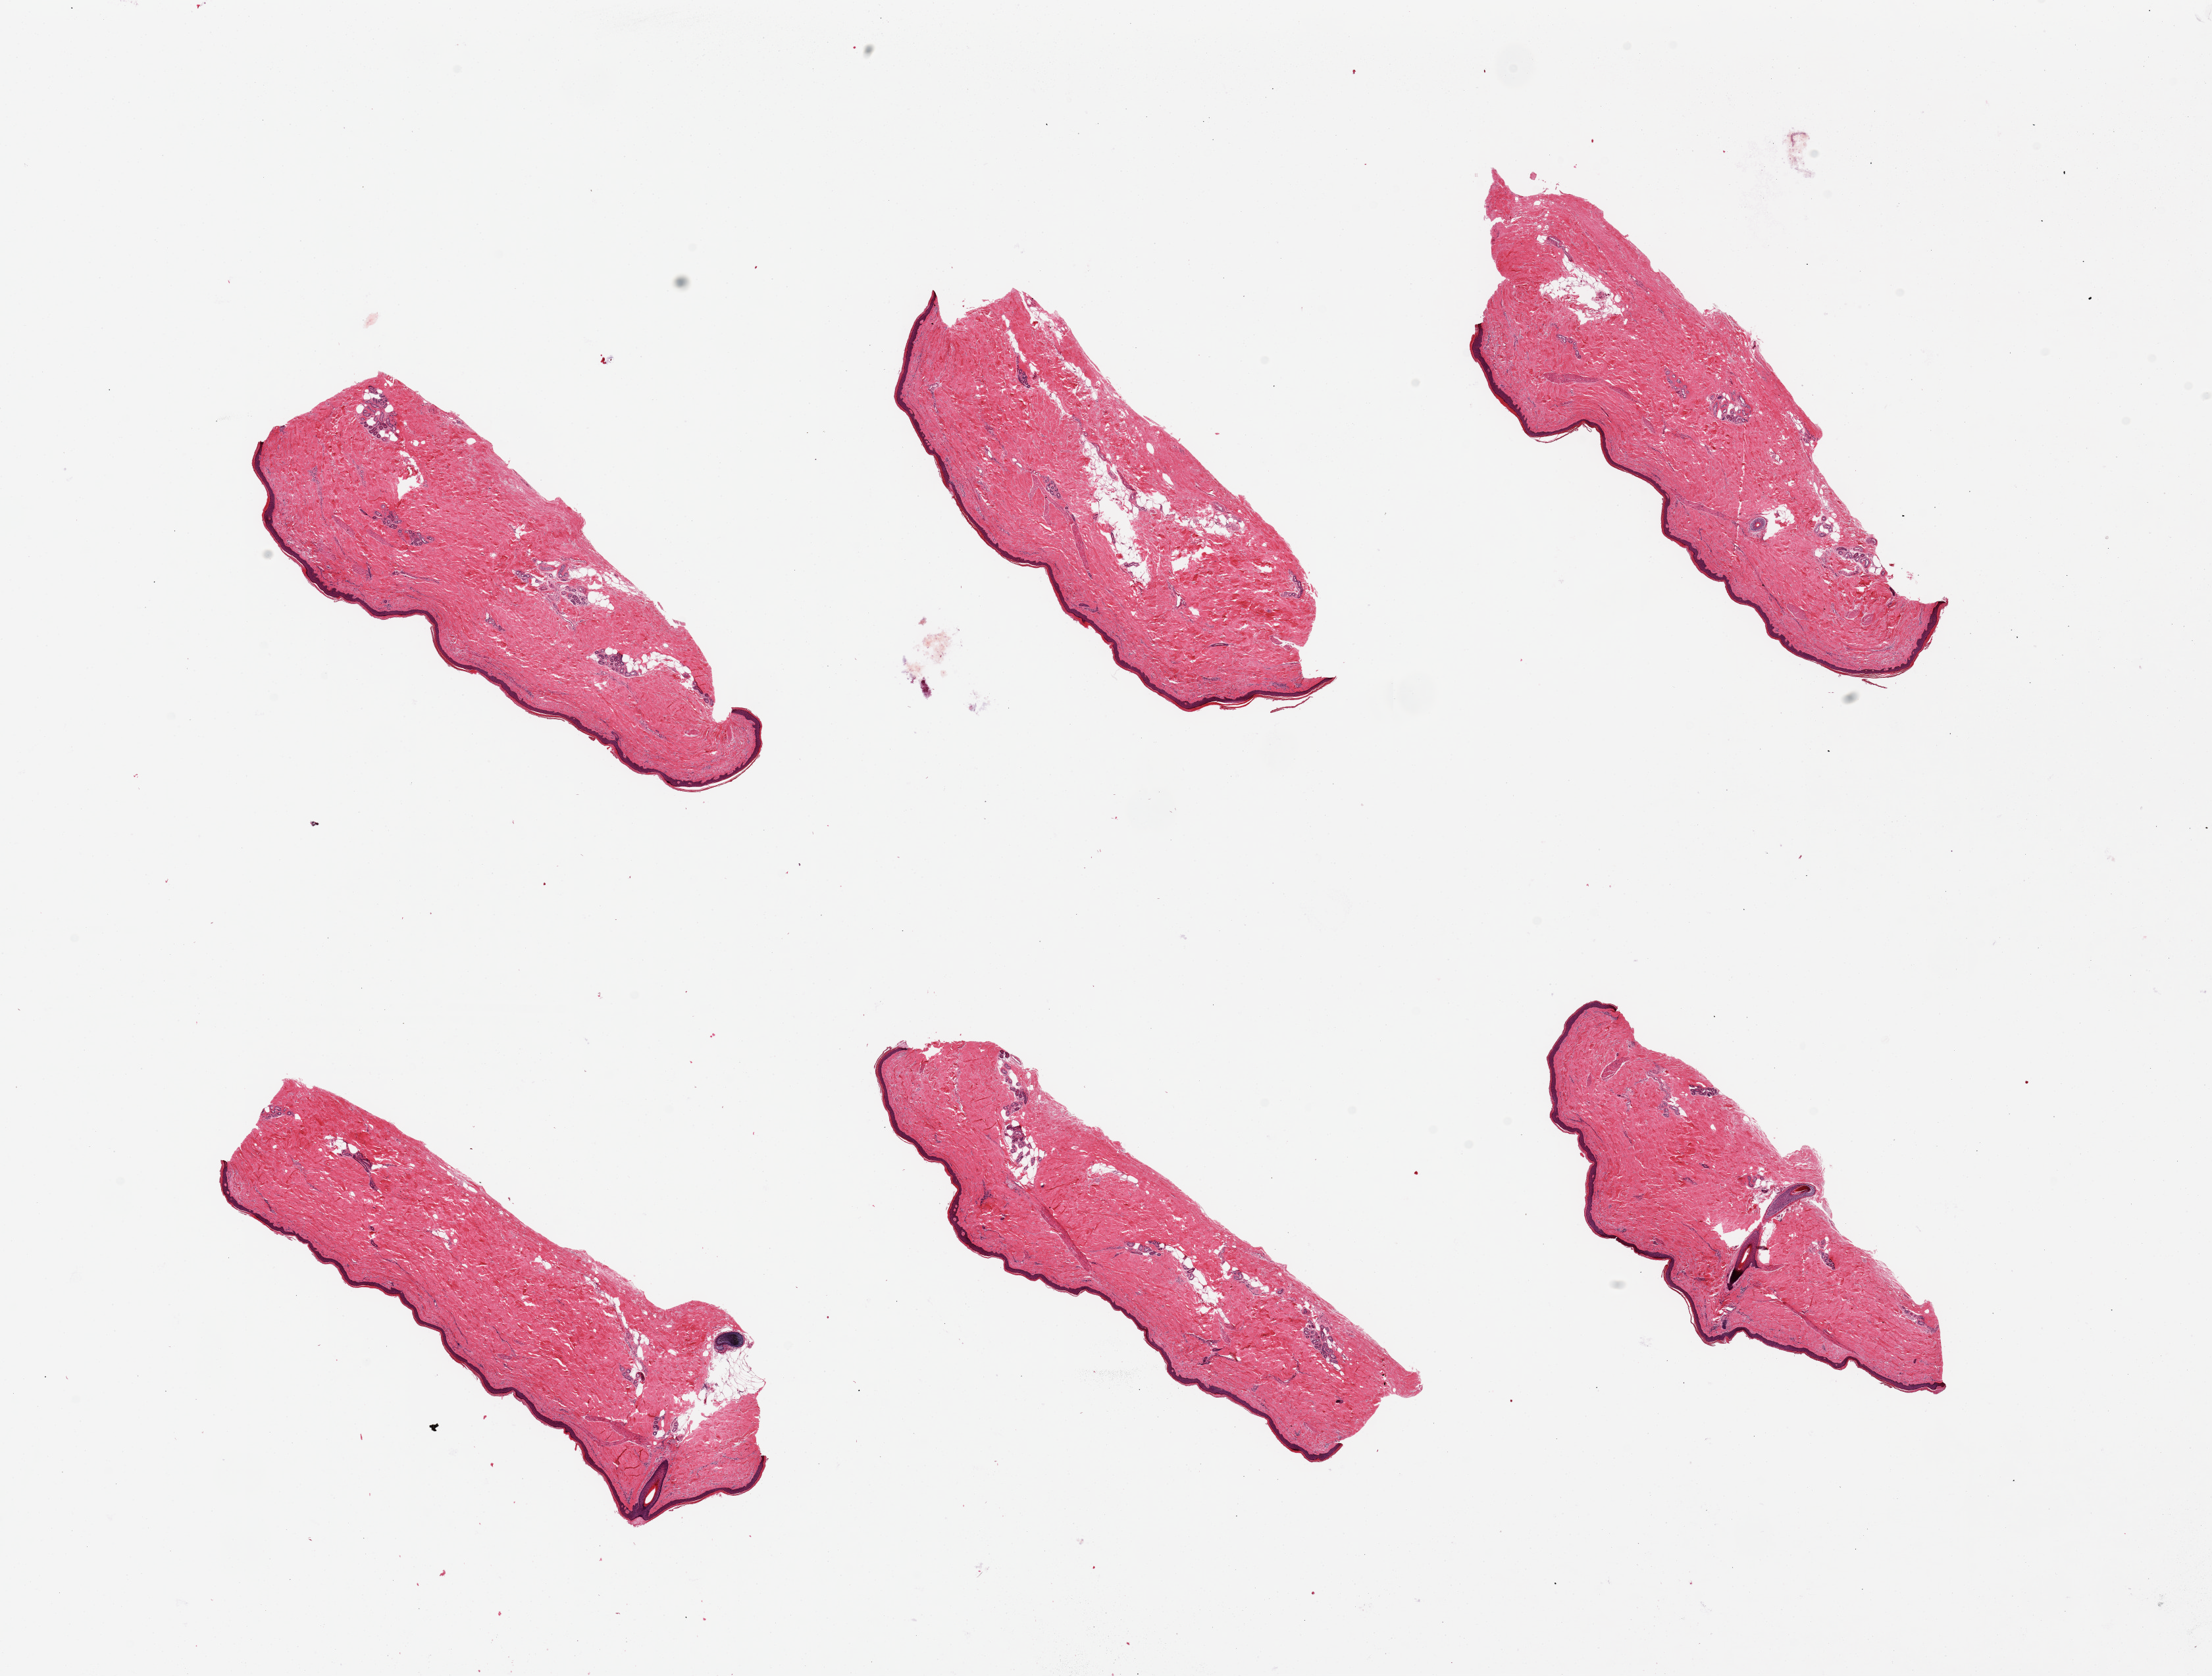
Digitized haematoxylin and eosin-stained section — low-resolution overview of the scanned area, about 26.6 x 20.1 mm; PAXgene-fixed, paraffin-embedded tissue; section of skin of lower leg (target tissue); donor tissue sample. Male donor.
Reviewer comment on this tissue sample: 6 pieces up to 8 x 3 mm. Well trimmed of subcutaneous adipose tissue.